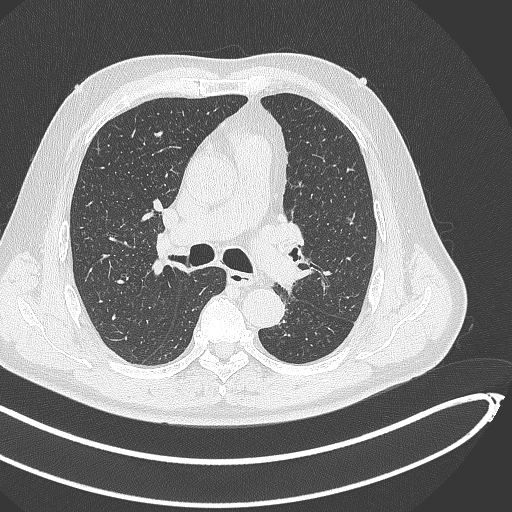
Chest CT, one axial slice. Position 286 of 468 along the scan axis. Reconstruction kernel B70f. Lung window (W 1500 / L -600 HU). 1 mm slice thickness. 512 × 512 image matrix, field of view 400 × 400 mm. Patient: male, 64 years. Case-level facts recorded for this patient, not image findings: clinical TNM (as recorded): T1c N0 M0; histopathological grade: G2.
Annotated regions visible in this slice (rectangle marked by the reading radiologist):
- lung tumour (recorded histology: squamous cell carcinoma): bounding box <274,267,312,293> (left, top, right, bottom; pixels)